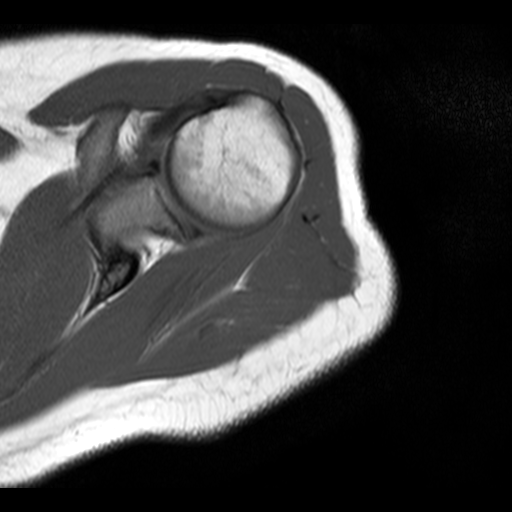
MRI of an extremity soft-tissue mass, one axial slice; position 15 of 20 along the scan axis; 4 mm slice thickness; 512 × 512 image matrix, field of view 150 × 150 mm. Female patient. From the clinical record (not read from this slice): histological type: malignant fibrous histiocytoma; grade: low; site of the primary tumour: left arm.
Outlined on this slice (outlined manually by an expert reader):
- gross tumour volume (mass): box from (x=224, y=304) to (x=253, y=325) px